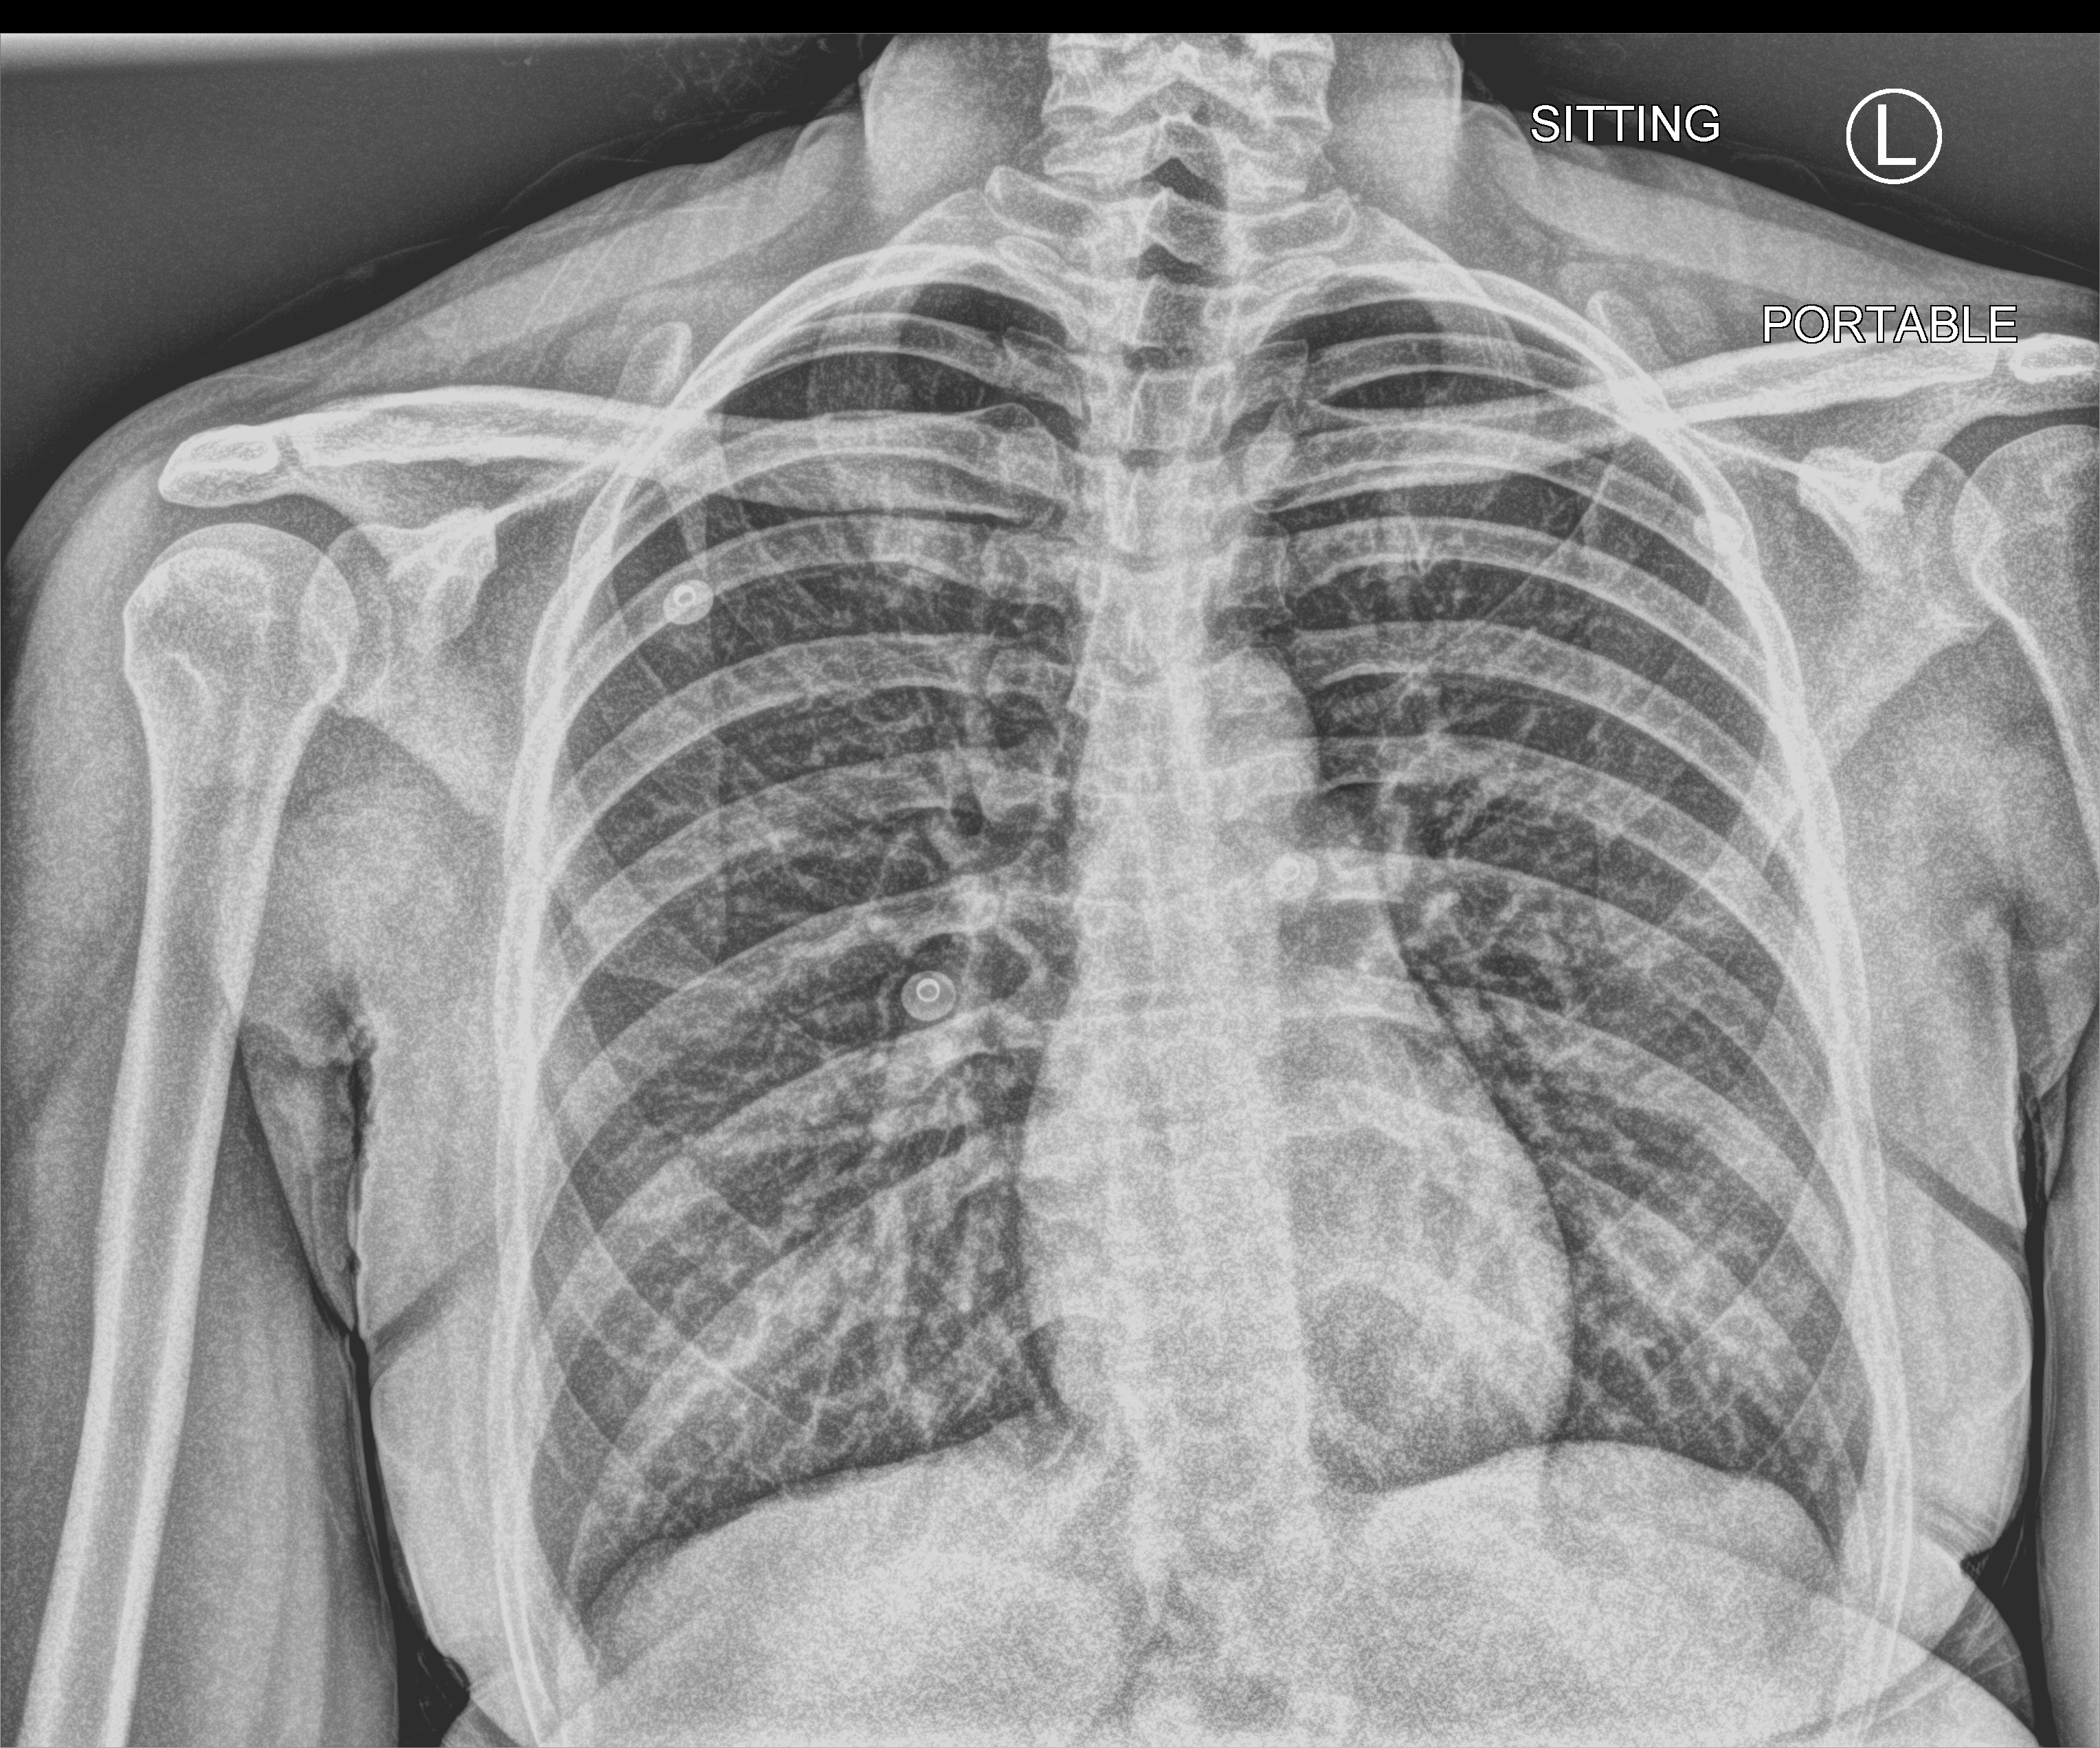
Bedside chest radiograph (computed radiography); anteroposterior (AP) projection. Patient hospitalised with COVID-19; female, aged 18–59 years.
From the hospital-stay record, not from the radiograph (when in the stay this image was taken is not recorded): mechanically ventilated during this hospital stay: no.